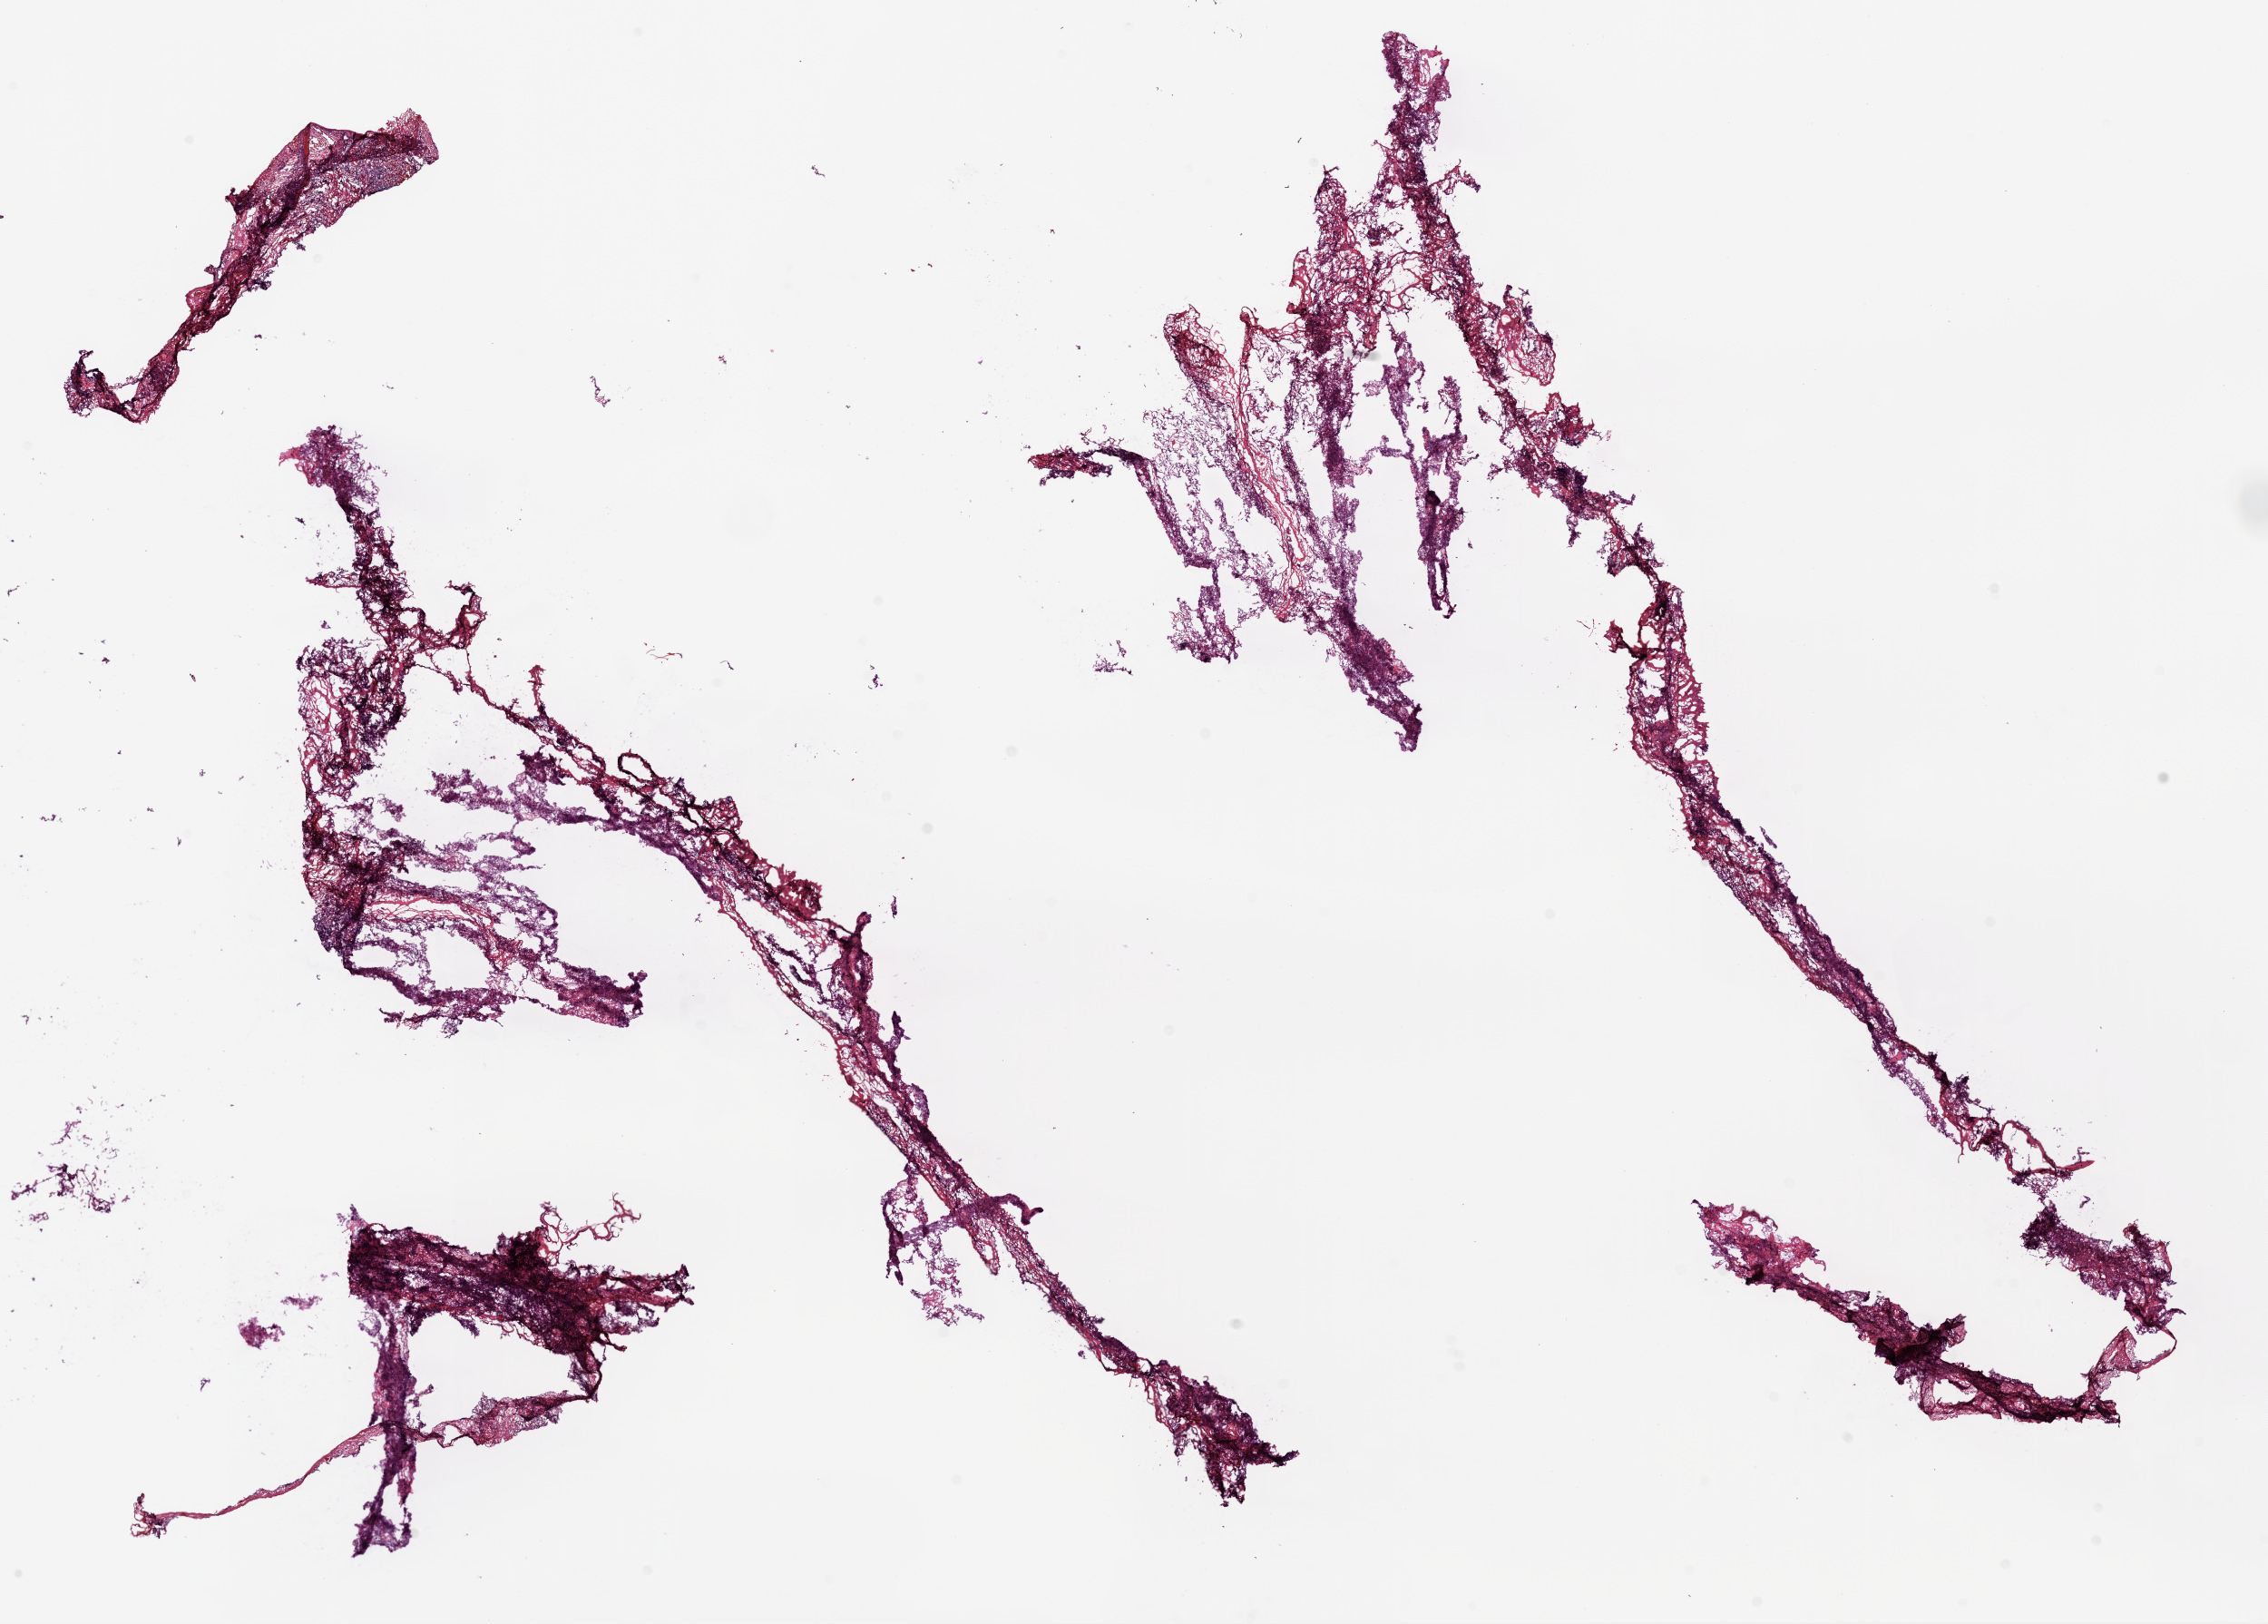
Digitized Hematoxylin and eosin (H&E) stained tissue section (whole slide) — shown as a low-resolution overview of the whole scanned area (about 20.1 x 14.4 mm). Frozen section from the bottom of the tissue portion. Sample: solid tissue normal (non-tumour tissue), lung. Male patient; age at initial diagnosis 39 years.
This section: solid tissue normal sample (biorepository sample class). Patient diagnosis: Squamous cell carcinoma, NOS.